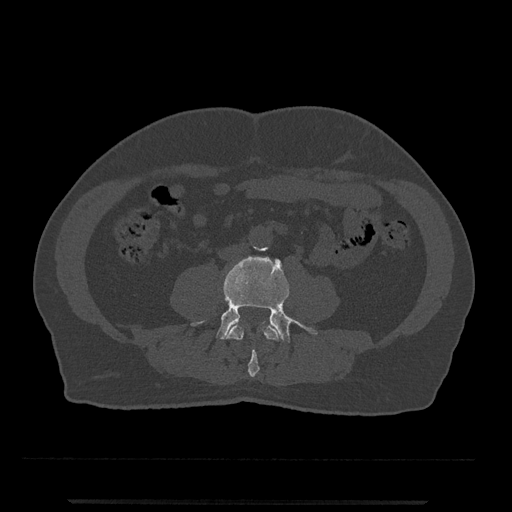
CT including the spine, one axial slice. Position 160 of 797 along the scan axis. Reconstruction kernel Br40s/3. Bone window (W 1800 / L 400 HU). 512 × 512 image matrix. Patient: male, 63 years. Case-level facts recorded for this patient, not image findings: primary cancer: prostate.
Outlined on this slice (semi-automatic segmentation, software-assisted and operator-edited):
- L3 vertebra: bounding box (x1, y1, x2, y2) in pixels: (227, 324, 280, 377)
- L4 vertebra: (191, 256, 318, 343)